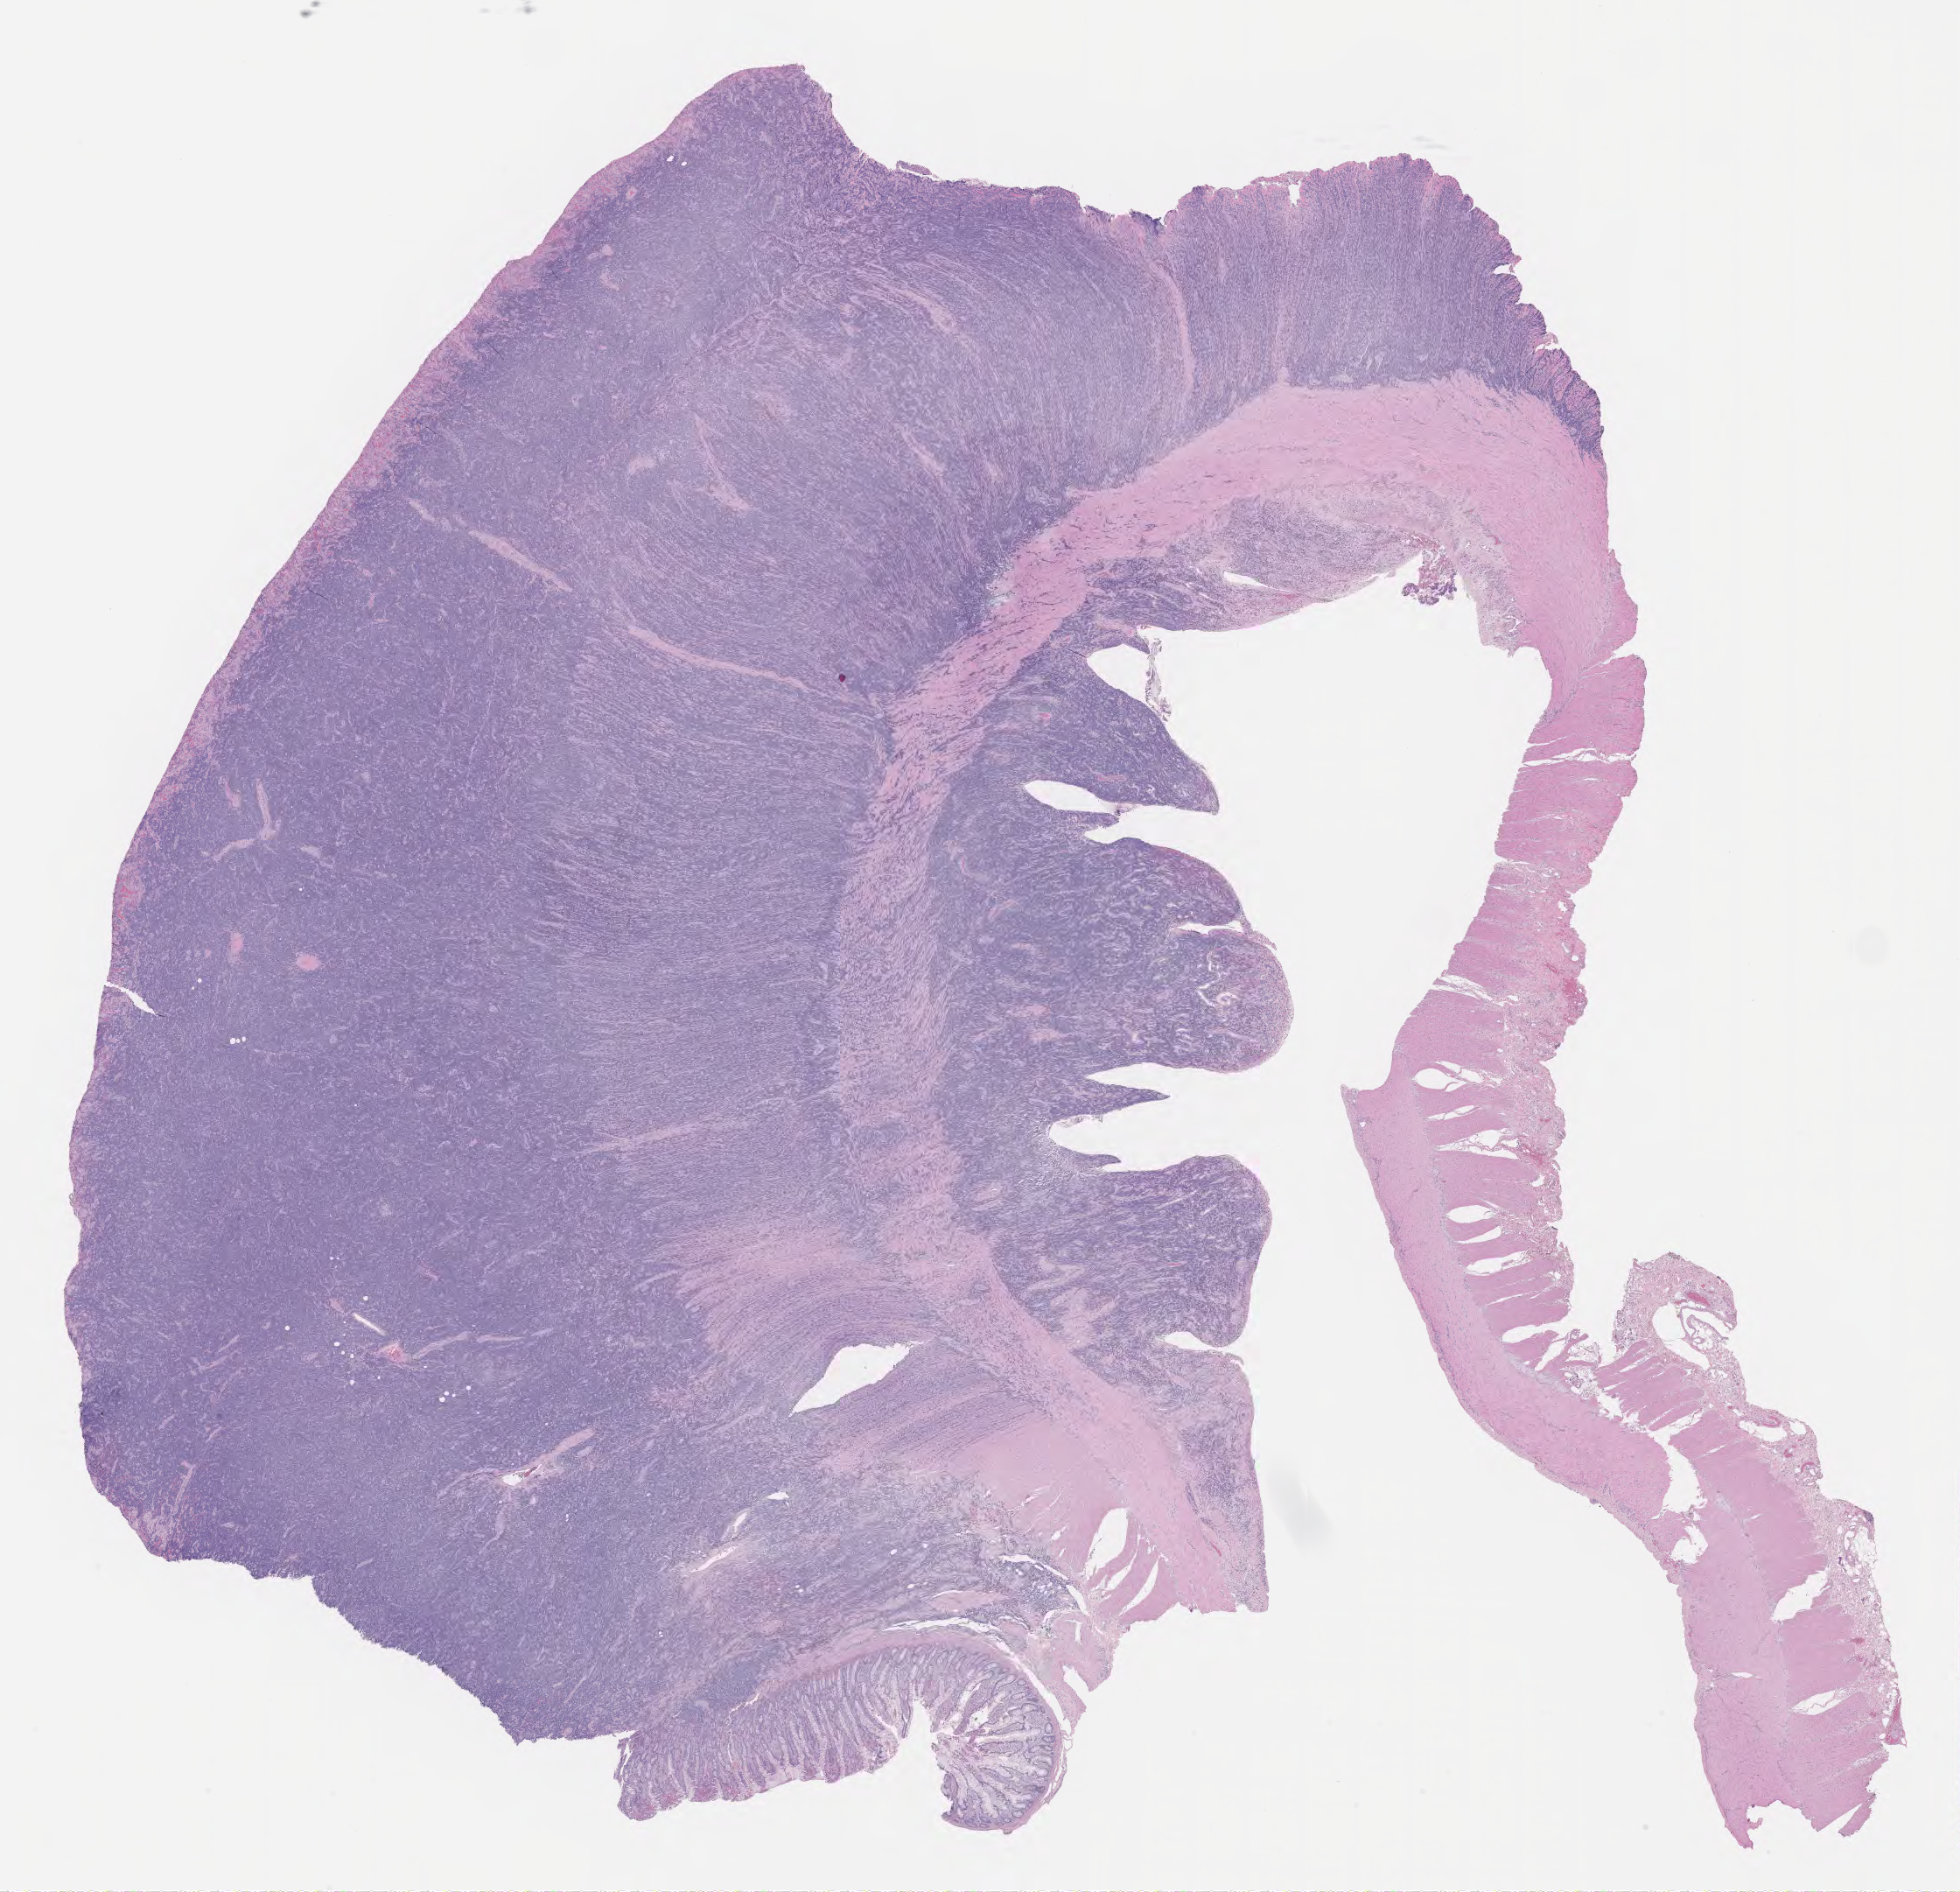
Hematoxylin and eosin (H&E) whole-slide image, shown as a low-resolution overview of the whole scanned area (about 18.1 x 17.5 mm), specimen: tumor tissue. Patient: male, age 27 years.
Diagnosis: Neoplasm, uncertain whether benign or malignant.